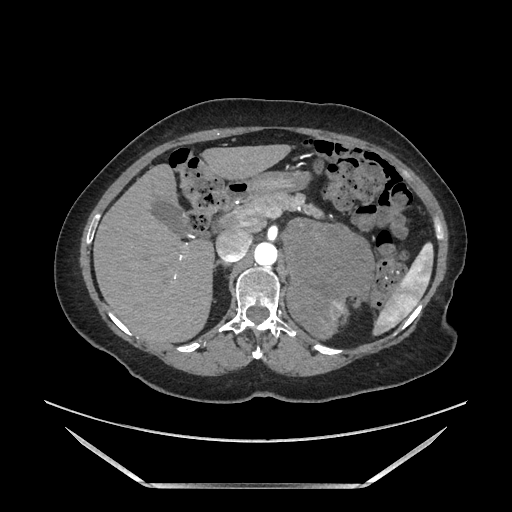
Contrast-enhanced abdominal CT, one axial slice; slice 112 of 205 in the series (ordered by position); soft-tissue window (W 400 / L 40 HU); 1.25 mm slice thickness; 512 × 512 image matrix, field of view 440 × 440 mm. Female patient. From the clinical record (not read from this slice): diagnosis: adrenocortical carcinoma; tumour side: left adrenal; tumour size at pathology: 12.5 cm; Ki-67 index: 39 %; stage (as recorded): 3.
Annotated regions visible in this slice (semi-automatically segmented with operator editing):
- mass: box from (x=287, y=225) to (x=368, y=336) px